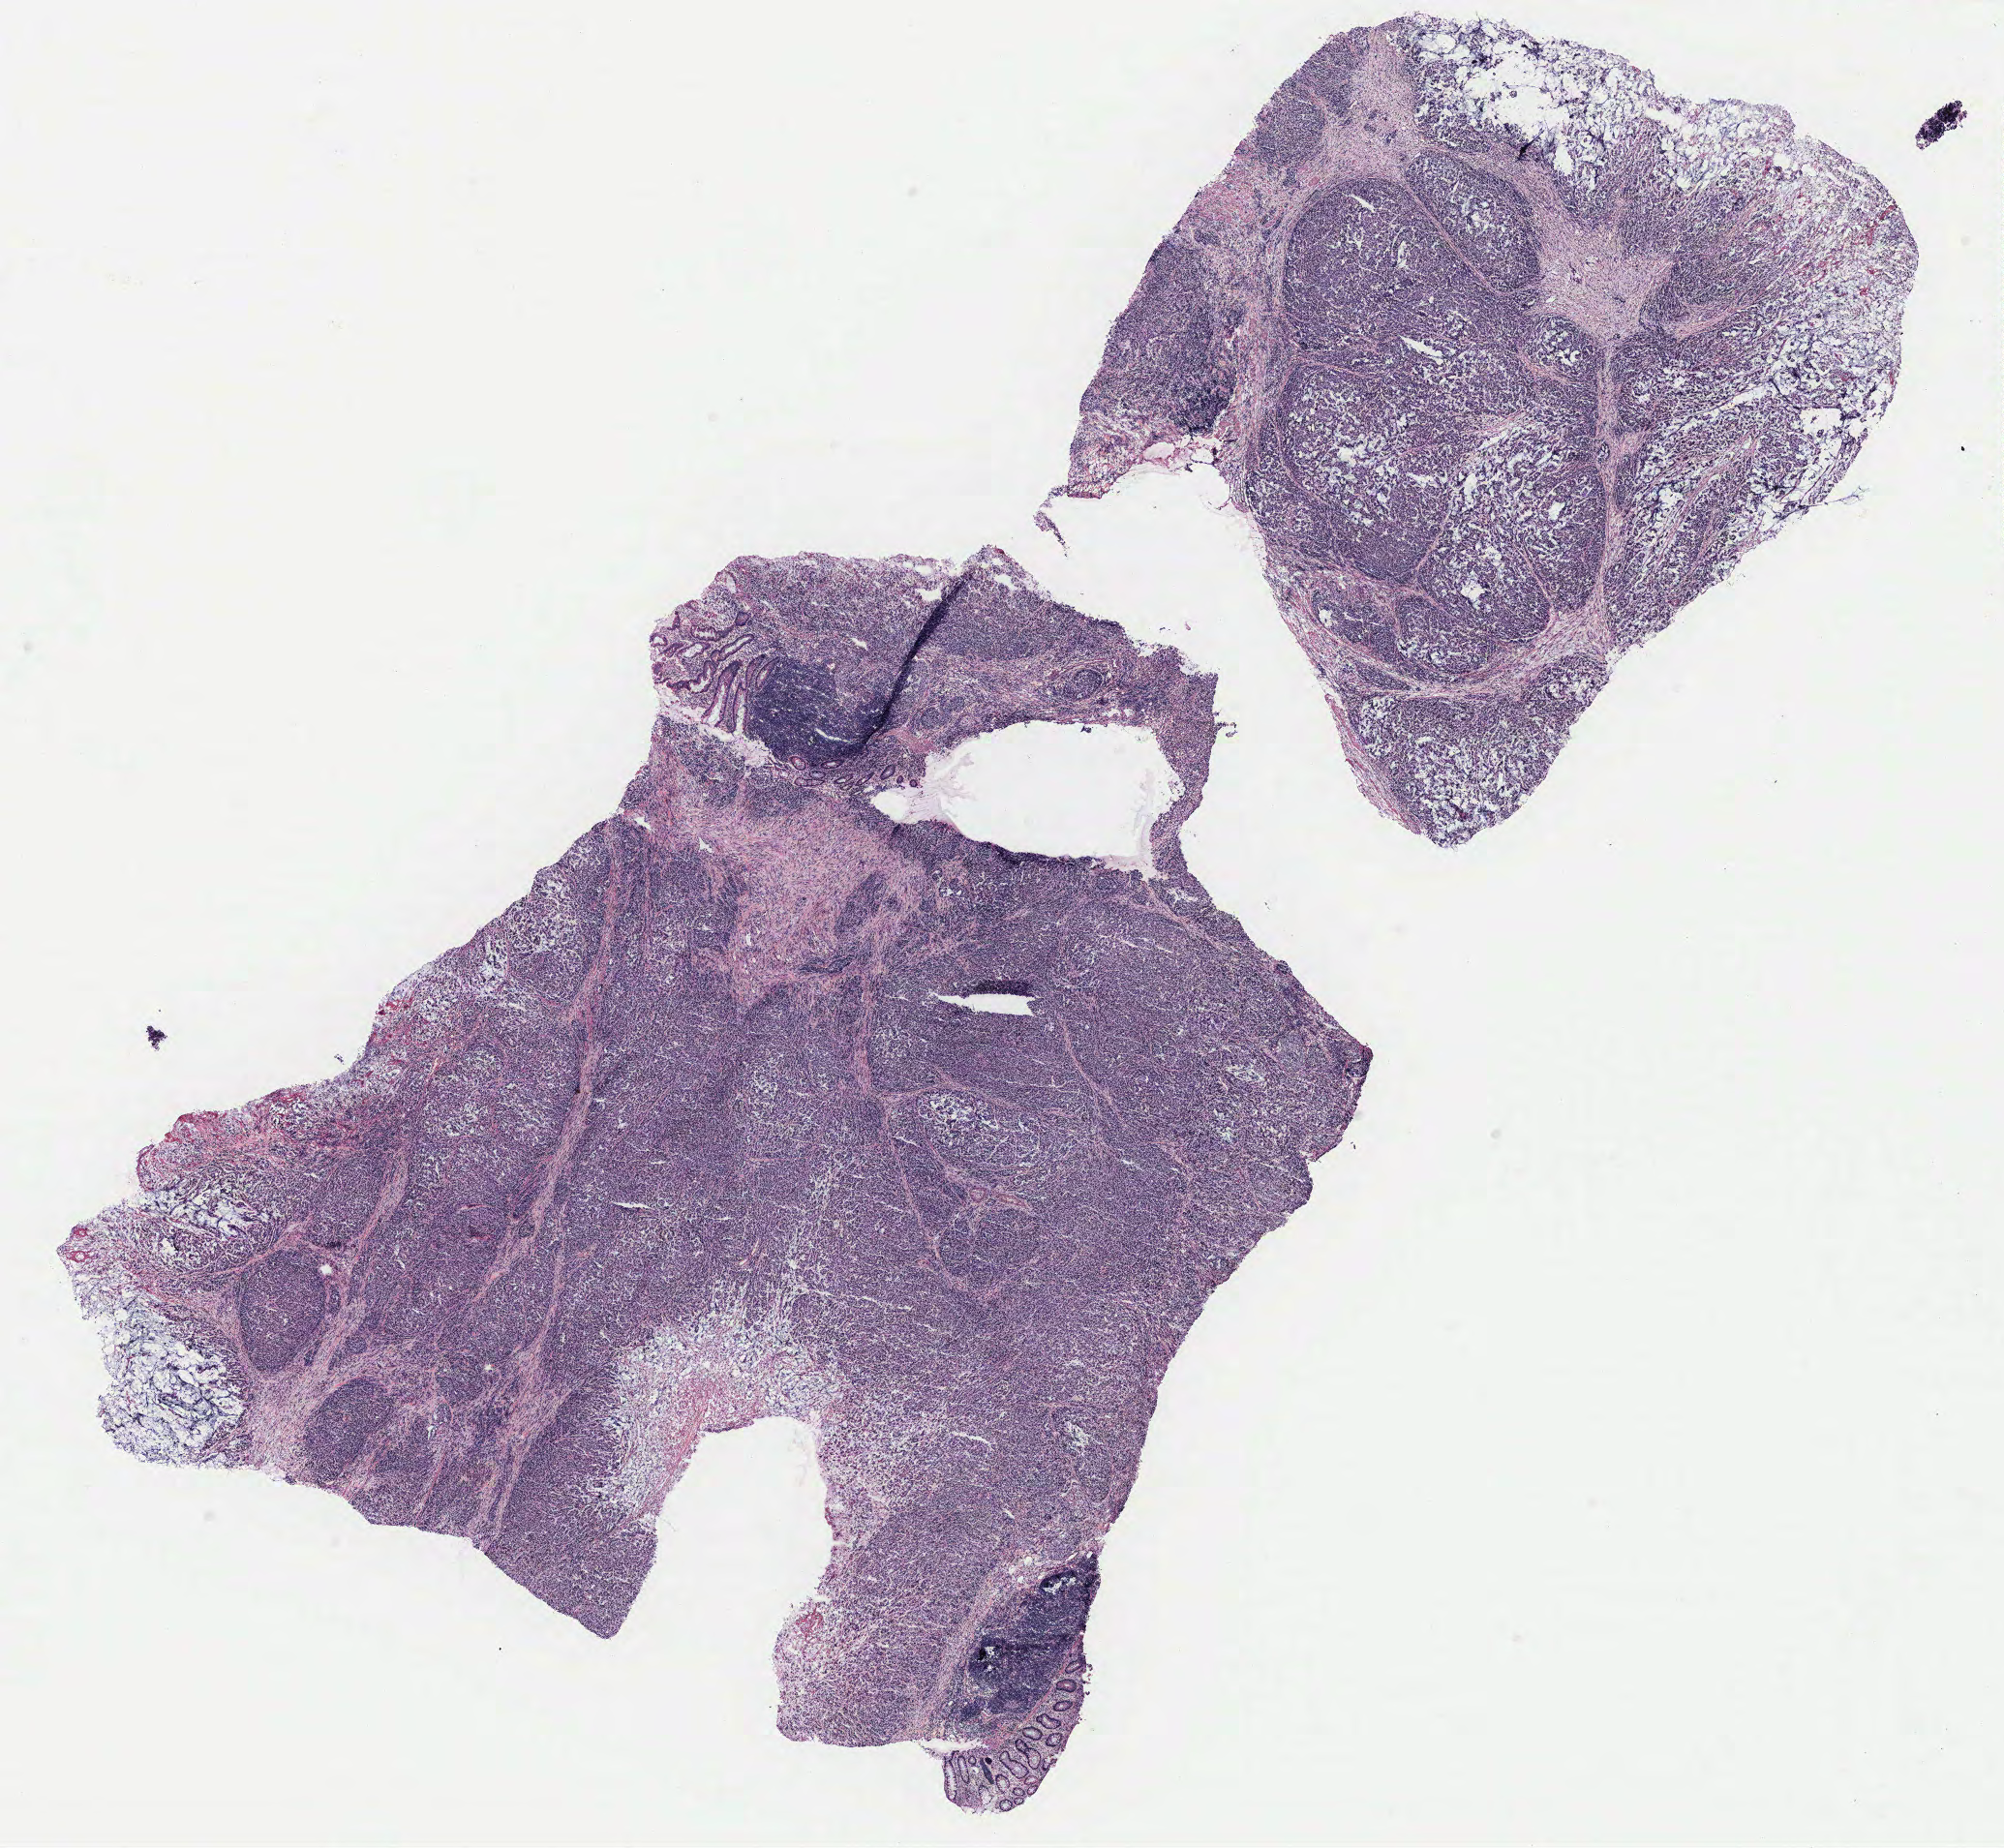
H&E whole-slide image, shown as a low-resolution overview of the whole scanned area (about 16.6 x 15.3 mm, from a 40x scan). Normal (non-tumour) tissue sample, colon. 83-year-old female patient.
This section: normal (non-tumour) tissue from the same patient. Patient diagnosis: Adenocarcinoma, NOS.